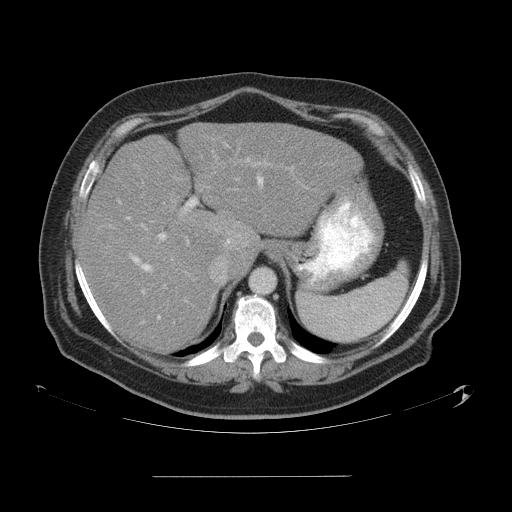
Contrast-enhanced abdominal CT, one axial slice. 120 kVp. Intravenous contrast given. Soft-tissue window (W 400 / L 40 HU). 5 mm slice thickness. 512 × 512 image matrix, field of view 480 × 480 mm. Male patient, age 63 years. Case-level facts recorded for this patient, not image findings: diagnosis: colorectal cancer liver metastases, imaged before liver resection.
Annotated regions visible in this slice (outlined manually by an expert reader):
- hepatic veins: bounding box <118,176,299,320> (left, top, right, bottom; pixels)
- liver: <80,123,358,352>
- planned liver remnant (the part of the liver to remain after resection): <80,196,217,352>
- portal vein (with intrahepatic branches): <139,155,271,294>
- liver metastasis: <216,225,246,252>